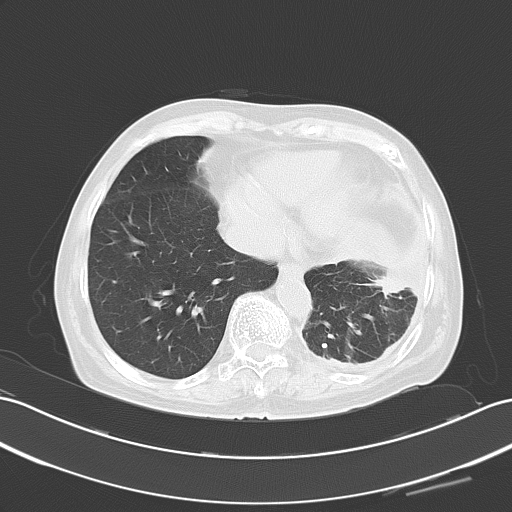
Chest CT, one axial slice. Slice 19 of 60 in the series (ordered by position). Reconstruction kernel B70f. 120 kVp. Lung window (W 1500 / L -600 HU). 5 mm slice thickness. 512 × 512 image matrix, field of view 353 × 353 mm. Female patient, age 82 years. Case-level facts recorded for this patient, not image findings: clinical TNM (as recorded): T1c N0 M1.
Annotated regions visible in this slice (bounding box drawn by a radiologist):
- lung tumour (recorded histology: adenocarcinoma): bounding box <372,262,418,301> (left, top, right, bottom; pixels)